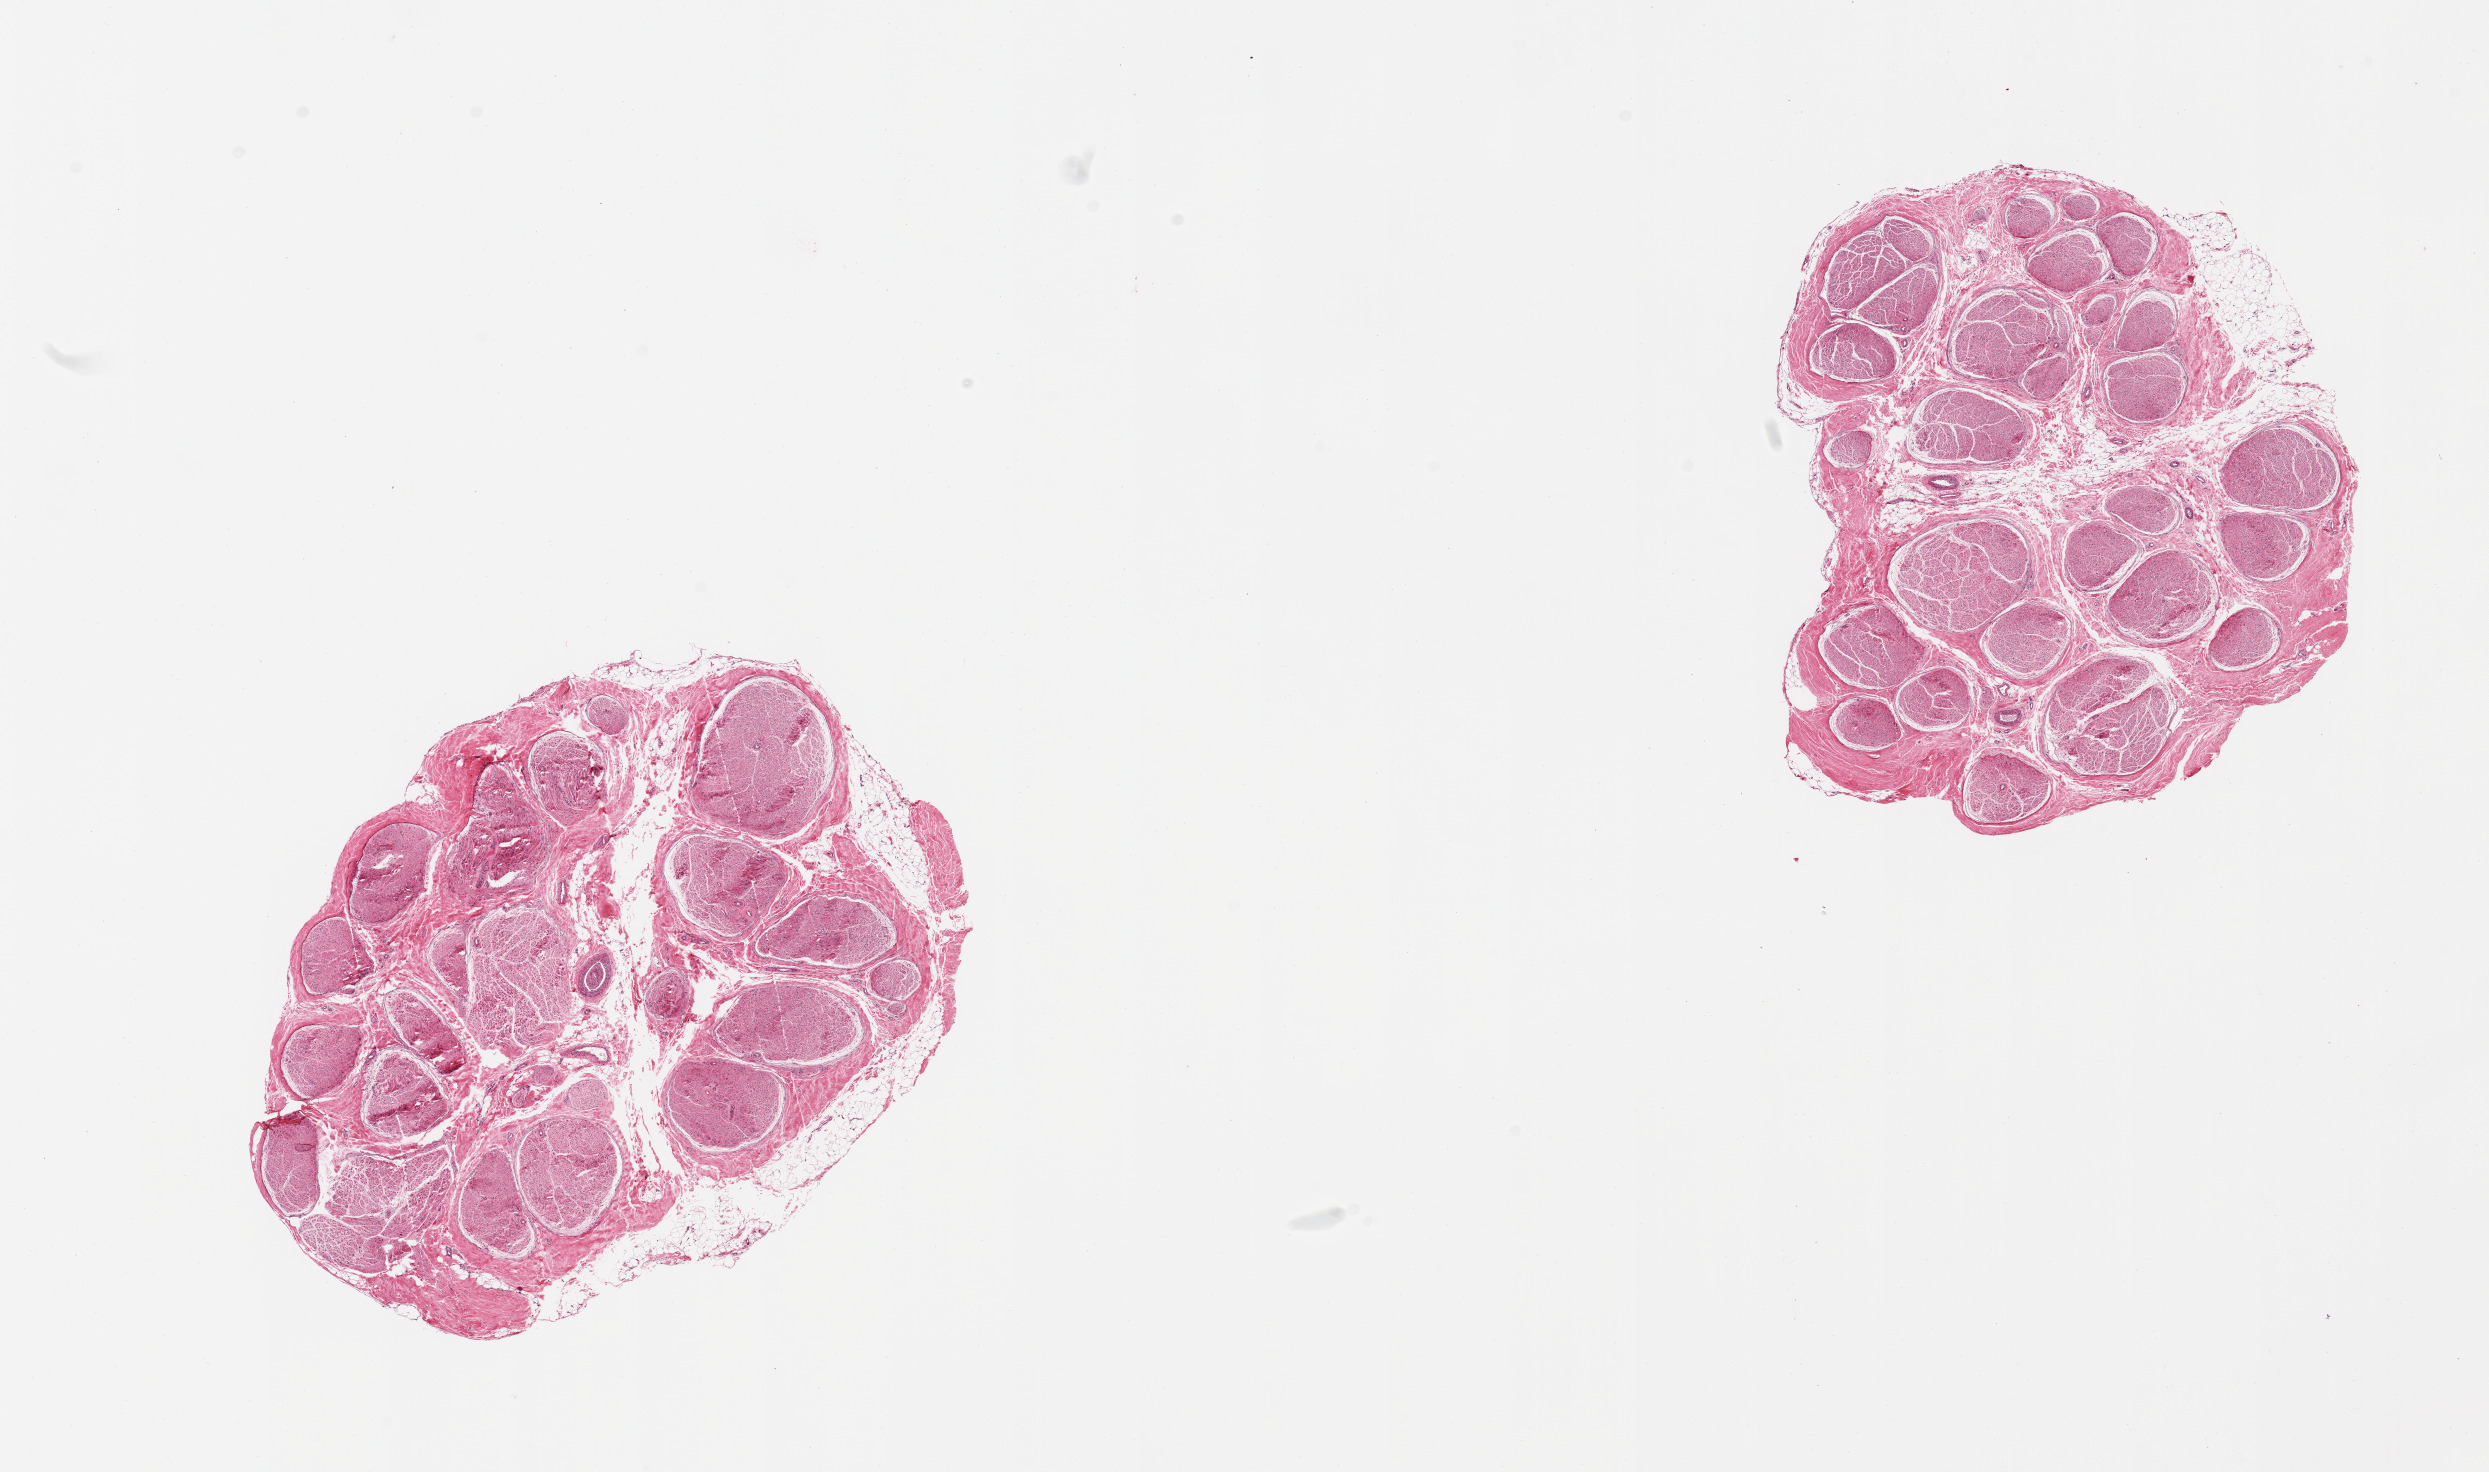
Digitized haematoxylin and eosin-stained section, brightfield — shown as a low-resolution overview of the whole scanned area (about 19.7 x 11.6 mm), PAXgene-fixed paraffin-embedded (PFPE) section, section of tibial nerve (target tissue), tissue donor sample. Donor: male.
Reviewer comment on this tissue sample: 2 pieces; 10% internal/external fat.